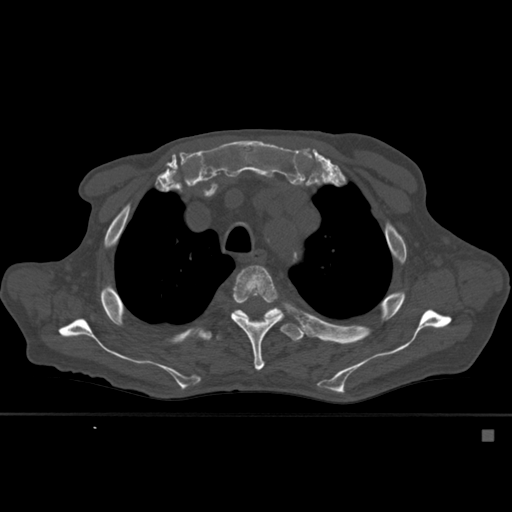
CT including the spine, one axial slice; slice 414 of 527 in the series (ordered by position); bone window (W 1800 / L 400 HU); 1.5 mm slice thickness; 512 × 512 image matrix, field of view 373 × 373 mm. Patient: male, 78 years. Case-level facts recorded for this patient, not image findings: primary cancer: prostate.
Annotated regions visible in this slice (semi-automatic segmentation, software-assisted and operator-edited):
- T4 vertebra: bounding box [x1, y1, x2, y2] px = [231, 265, 283, 371]
- T5 vertebra: [216, 307, 307, 342]